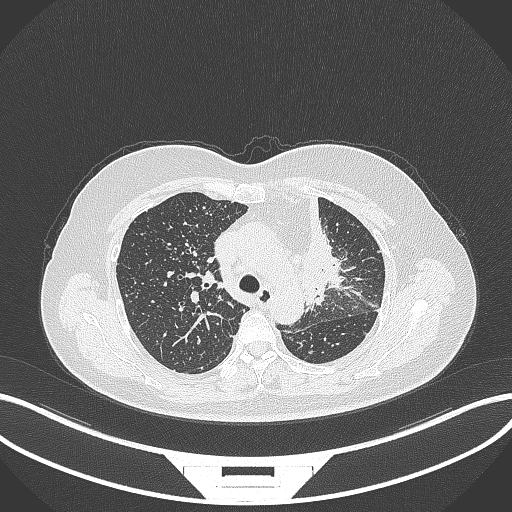
Chest CT, one axial slice; position 234 of 348 along the scan axis; reconstruction kernel B70f; lung window (W 1500 / L -600 HU); 1 mm slice thickness; 512 × 512 image matrix, field of view 400 × 400 mm. Female patient, age 49 years. Case-level facts recorded for this patient, not image findings: clinical TNM (as recorded): T1c N0 M1.
Annotated regions visible in this slice (rectangle marked by the reading radiologist):
- lung tumour (recorded histology: adenocarcinoma): bounding box (x1, y1, x2, y2) in pixels: (290, 196, 341, 311)